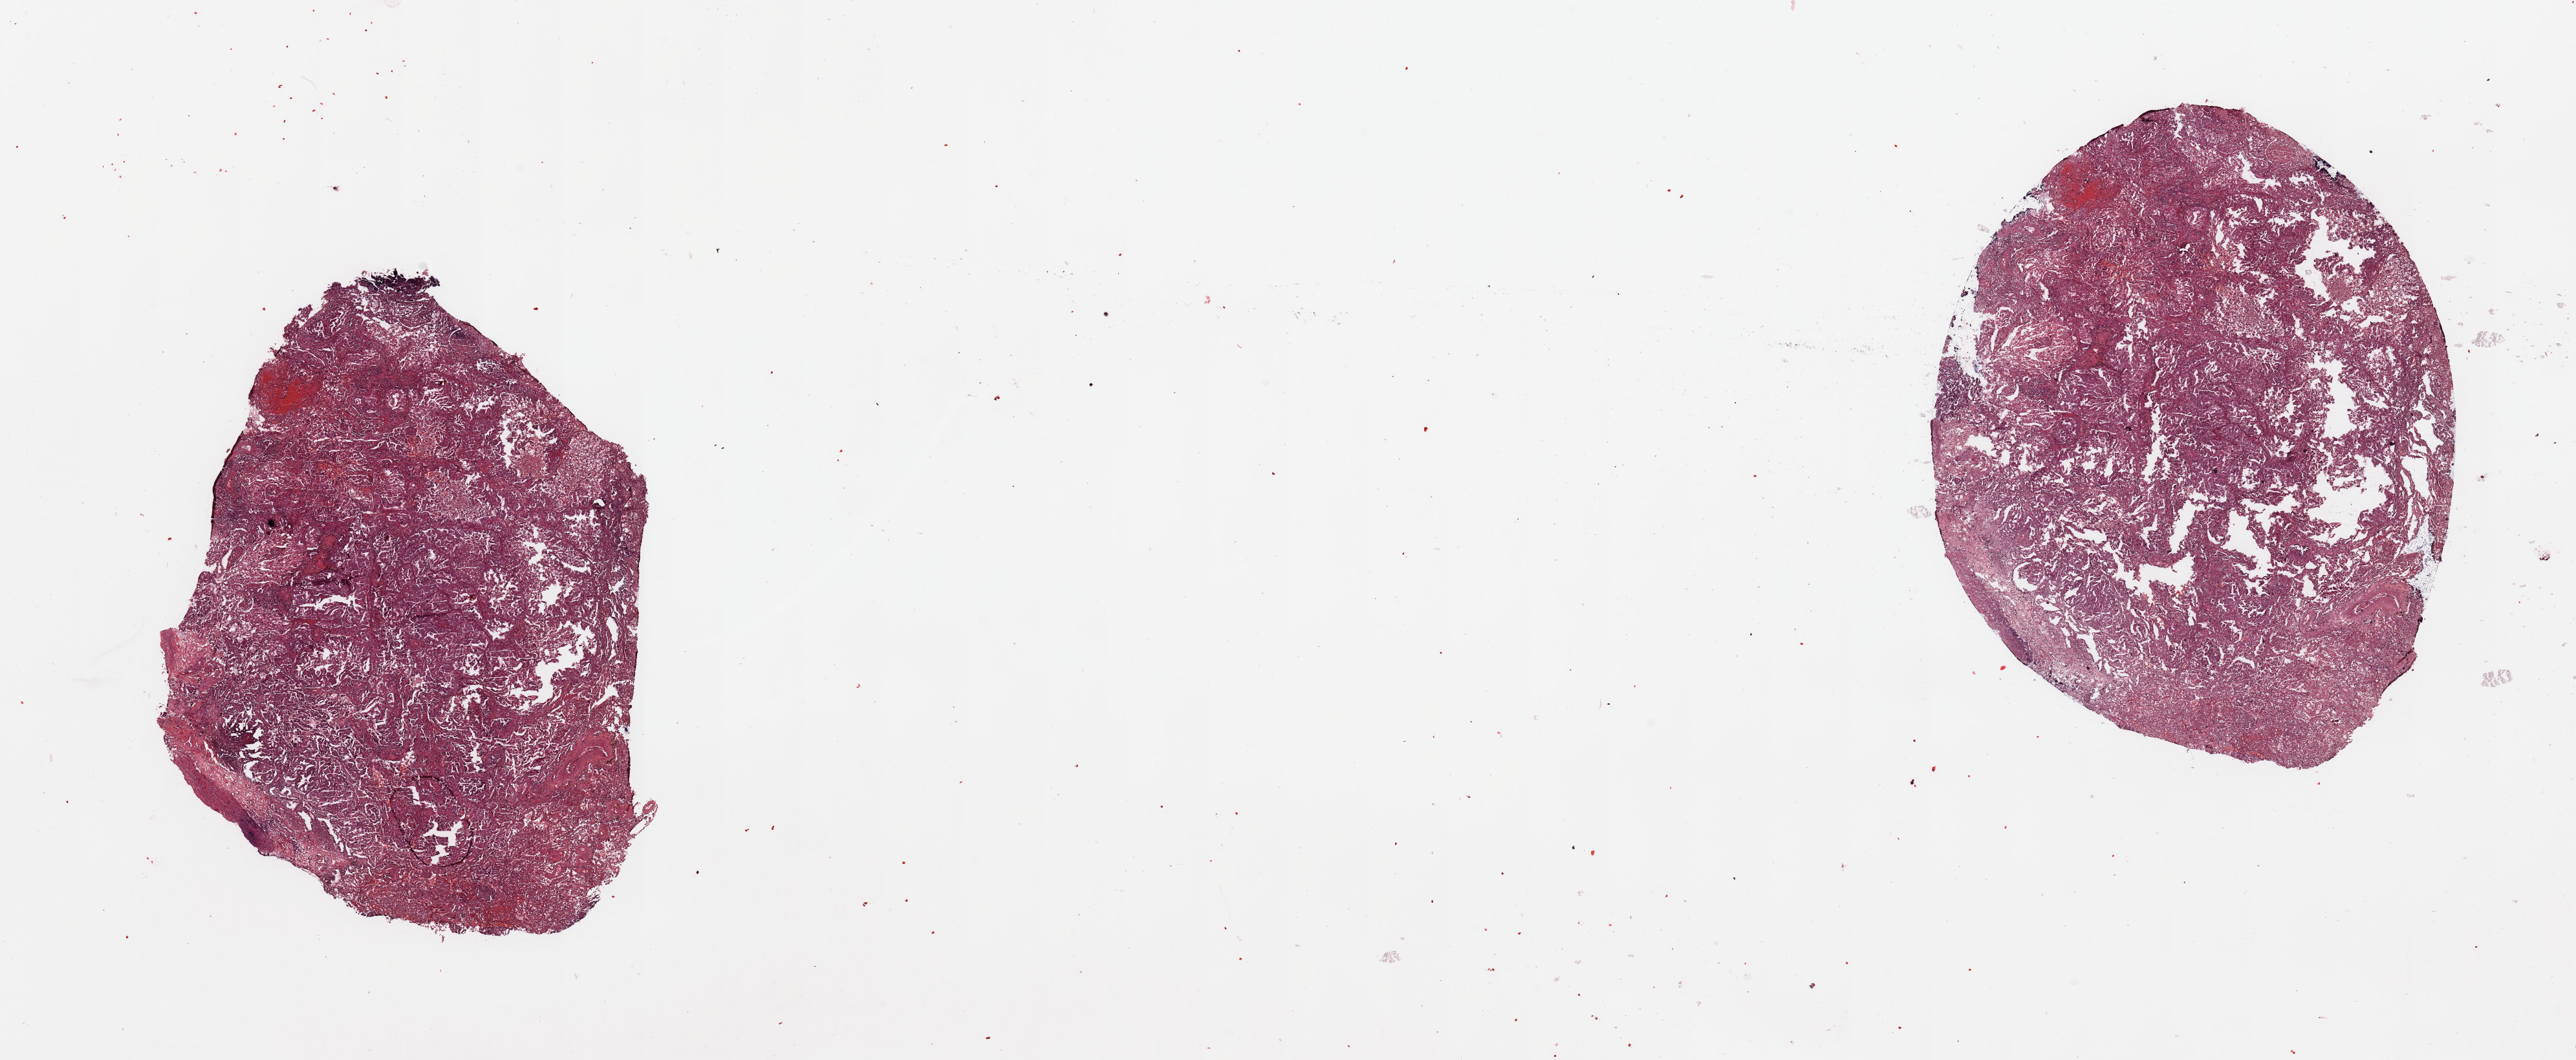
Digitized H&E tissue section (whole slide), whole scanned area (about 31.5 x 13.0 mm) shown as a low-resolution overview, lung, tumour tissue. 59-year-old male patient. Histologic grade: G2 (moderately differentiated).
AJCC pathologic stage: IIIA. Histologic diagnosis: Adenocarcinoma, NOS.